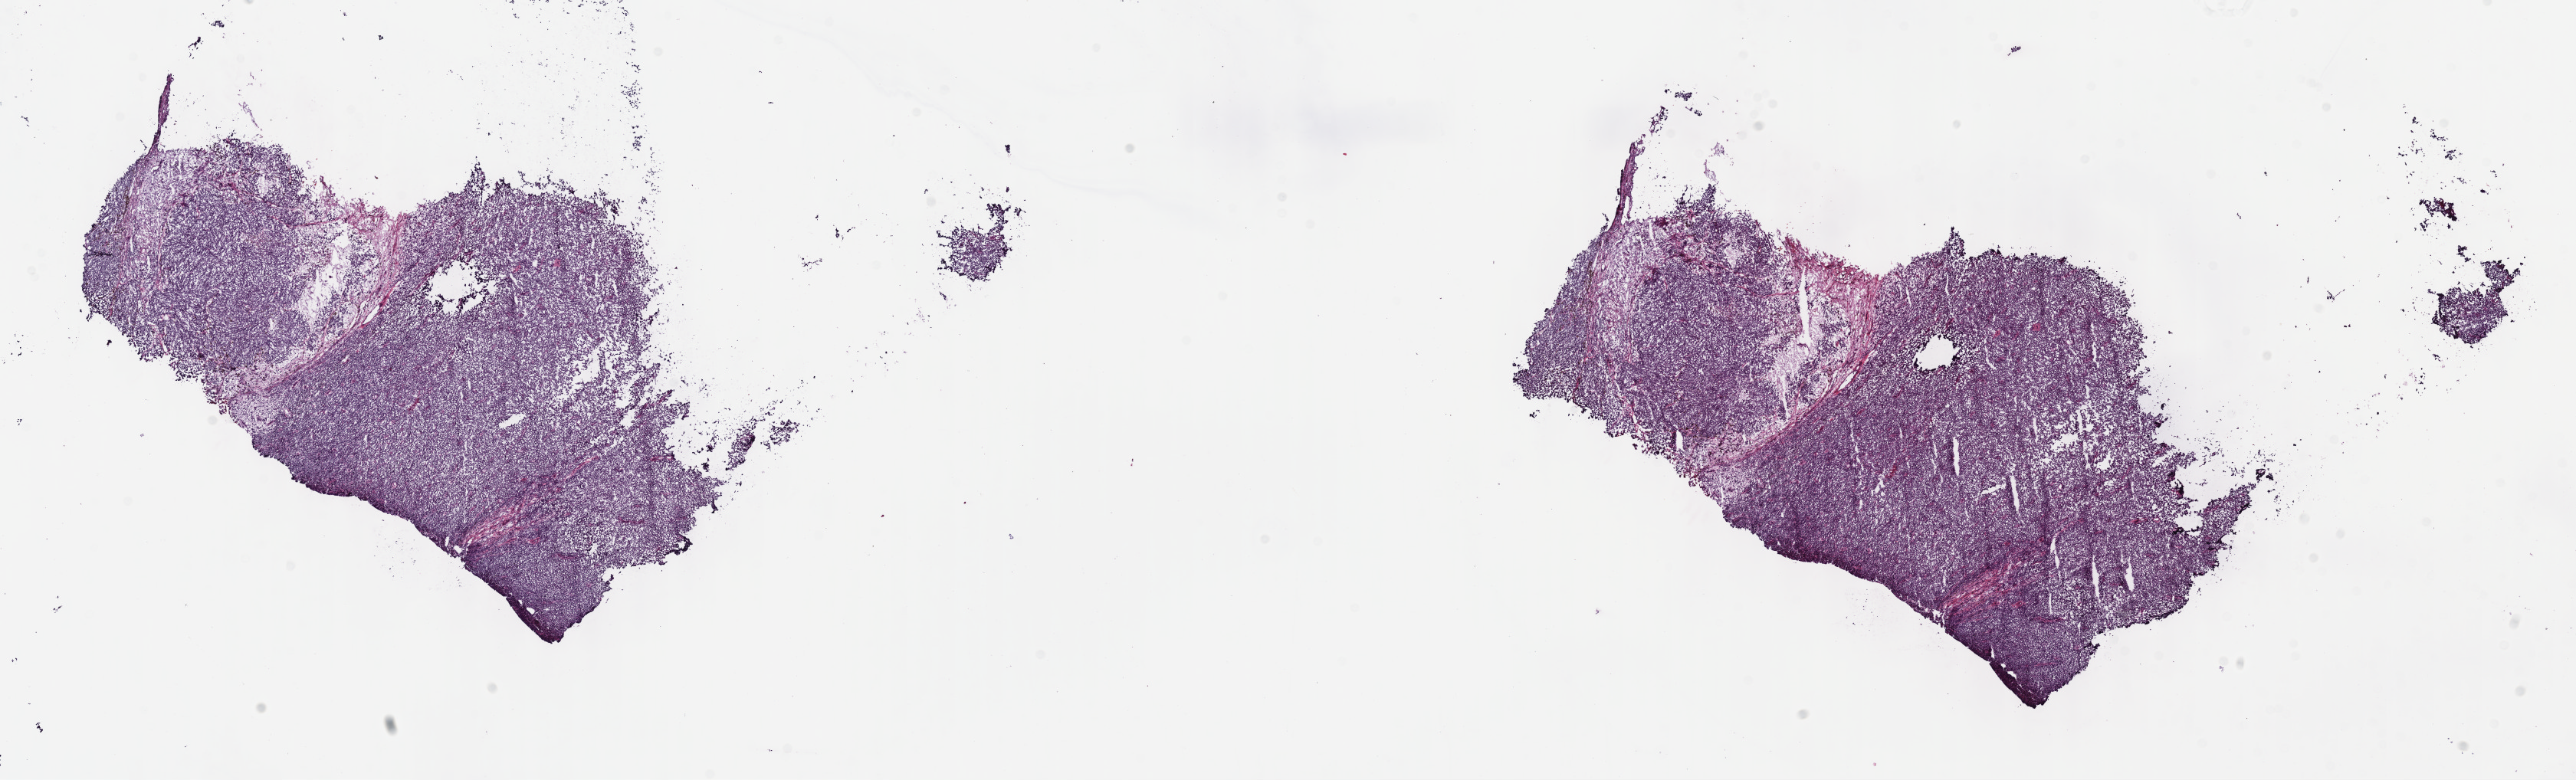
Digitized H&E tissue section (whole slide) — a low-resolution overview of the entire scanned area, about 27.2 x 8.2 mm; frozen section; sample: primary tumour, skin. Female patient; age at initial diagnosis 66 years. Slide review estimates, as recorded: tumour cells 100%, tumour nuclei 80%, normal cells 0%, stromal cells 0%, necrosis 0%. Inflammatory infiltration, as recorded: lymphocyte infiltration 2%, monocyte infiltration 0%, neutrophil infiltration 0%.
• AJCC pathologic stage: IIB (7th edition)
• pathologic diagnosis: Malignant melanoma, NOS